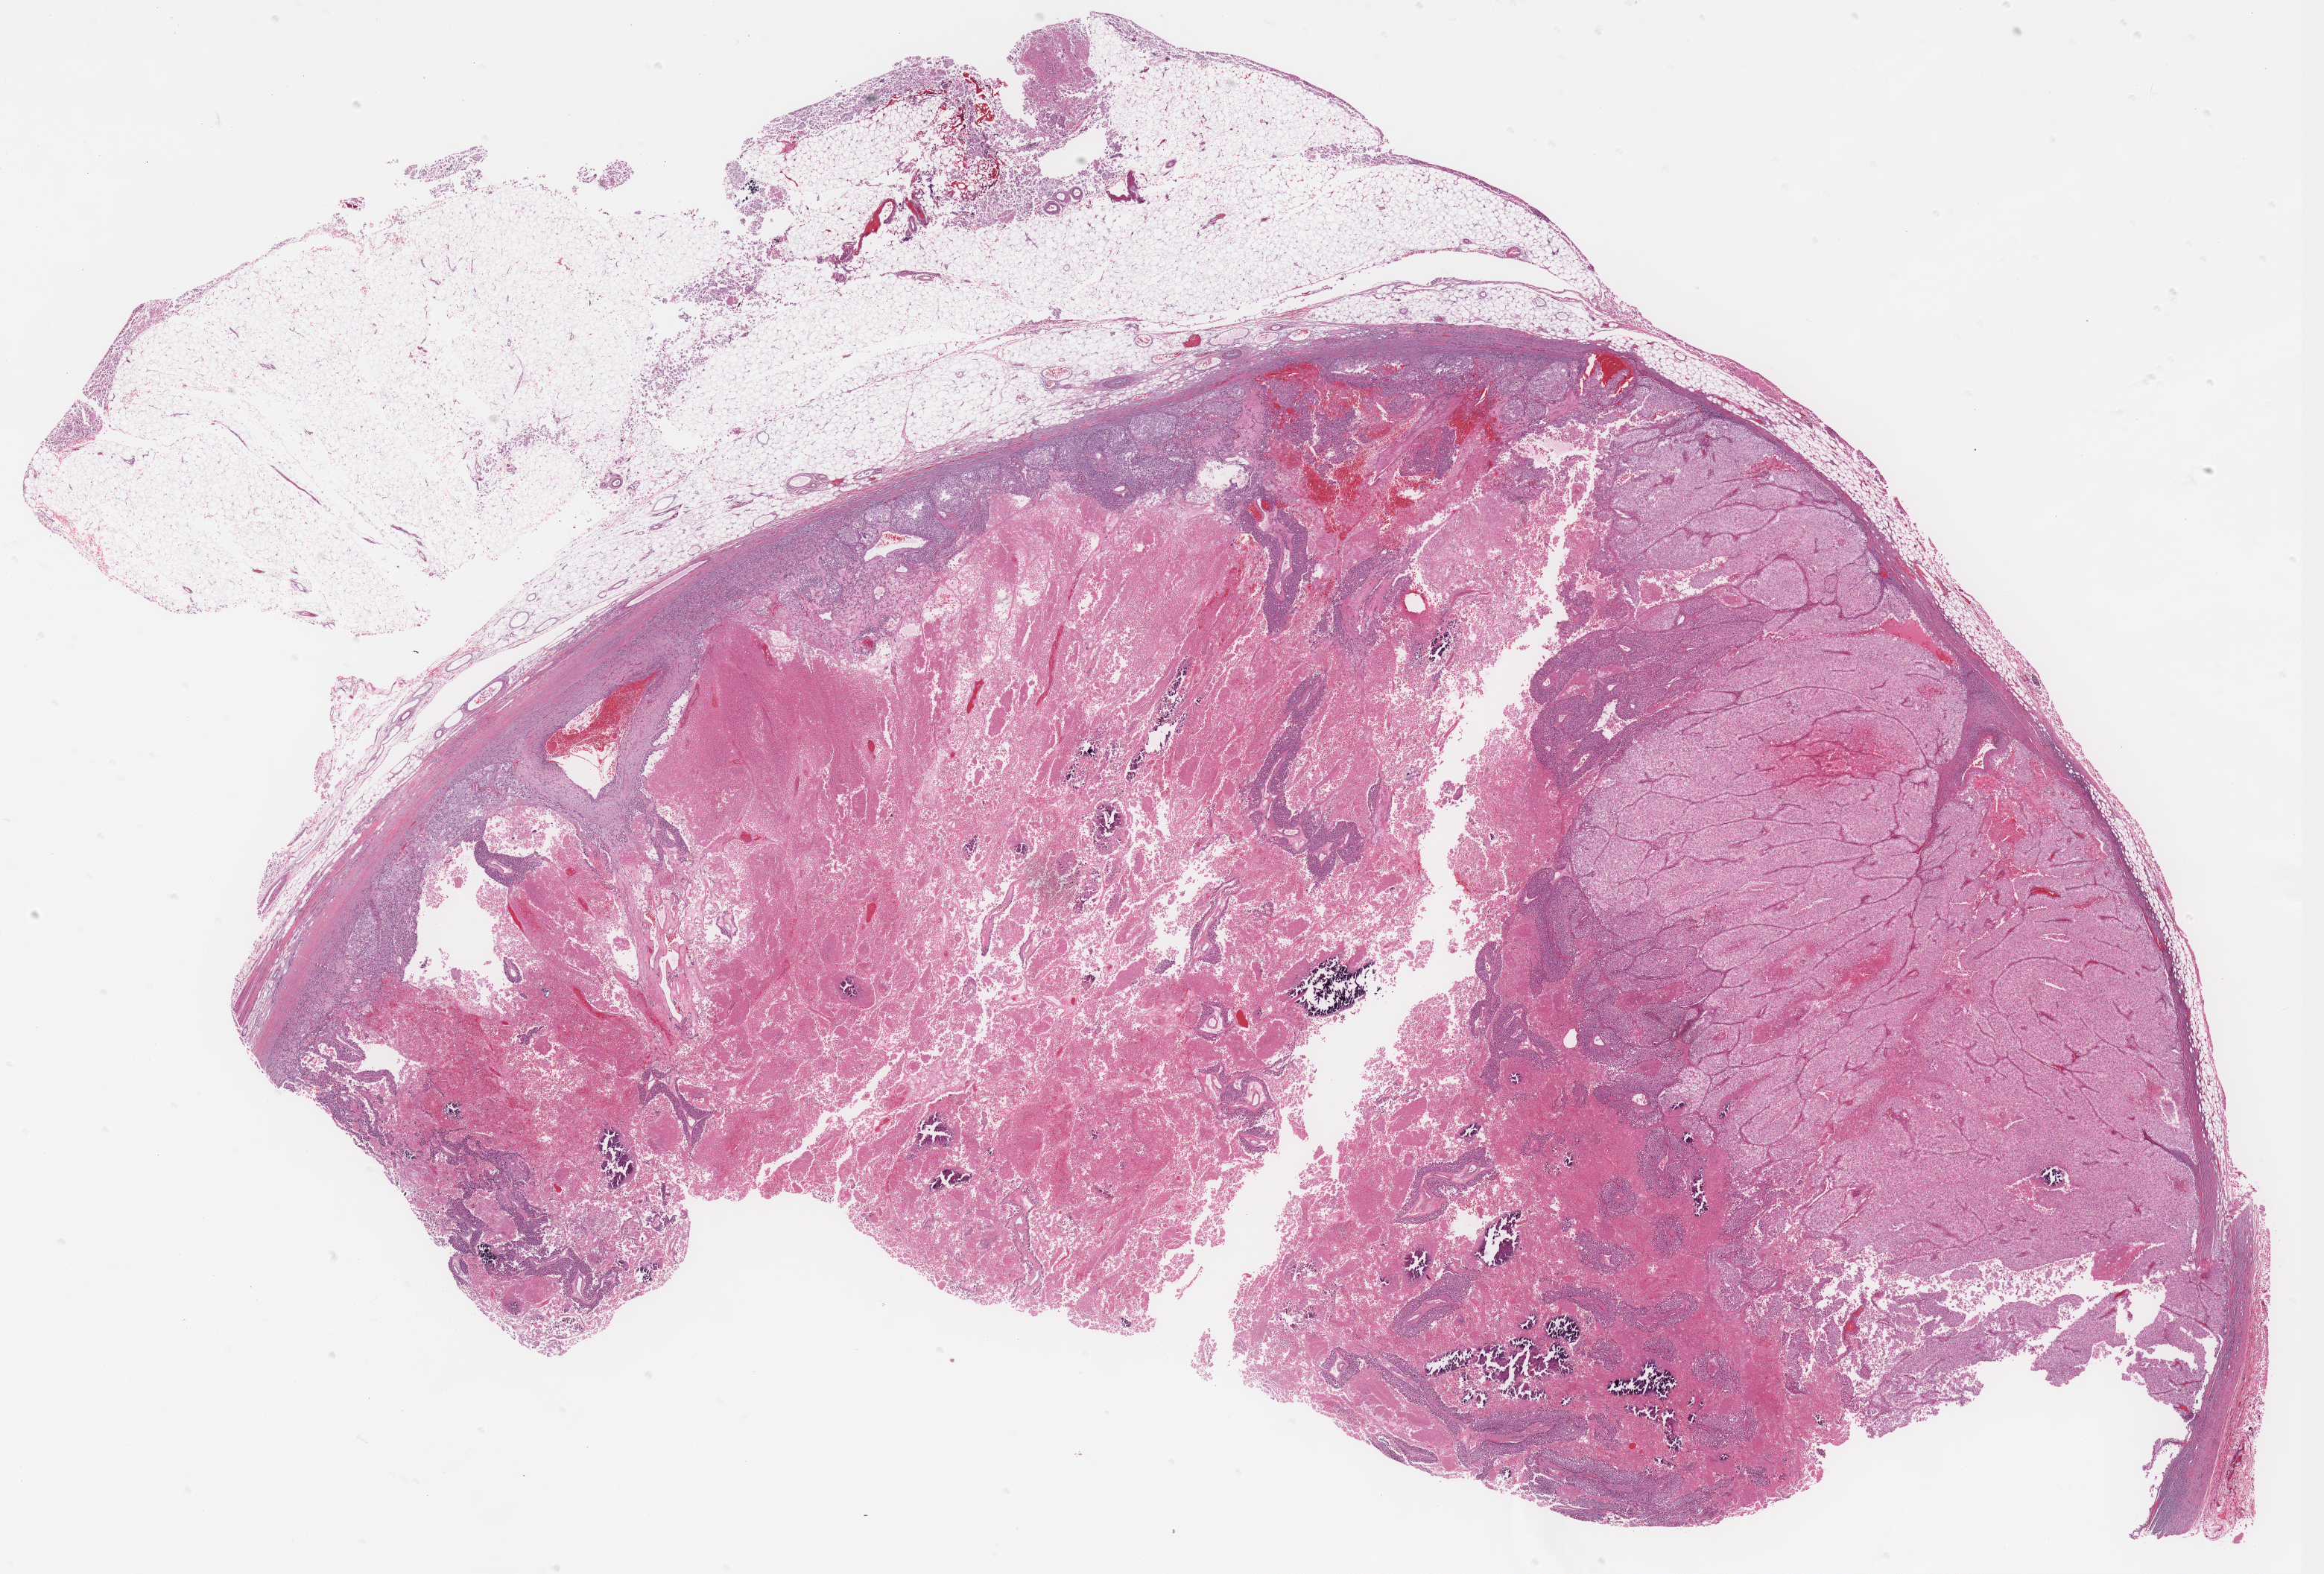
H&E-stained whole-slide image — a low-resolution overview of the entire scanned area, about 24.9 x 16.9 mm (from a 40x scan), FFPE section, kidney, primary tumour sample. Patient: male, age at initial diagnosis 41 years.
Histologic diagnosis: Renal cell carcinoma, chromophobe type.